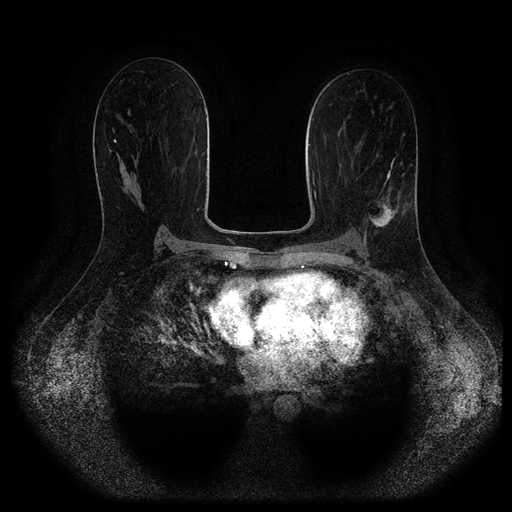
Breast MRI (dynamic contrast-enhanced, multi-phase), one axial slice. Dynamic contrast-enhanced series, time point 2 of 5 at this slice position (early post-contrast). 1.5 T. TE 2.6 ms, TR 5.3 ms. 2 mm slice thickness. 512 × 512 image matrix. Patient: female, 45 years.
Annotated regions visible in this slice (semi-automatic segmentation, software-assisted and operator-edited):
- breast lesion (labelled 'tumour' in the annotation; benign lesions carry a separate 'benign' label): box from (x=367, y=199) to (x=398, y=230) px